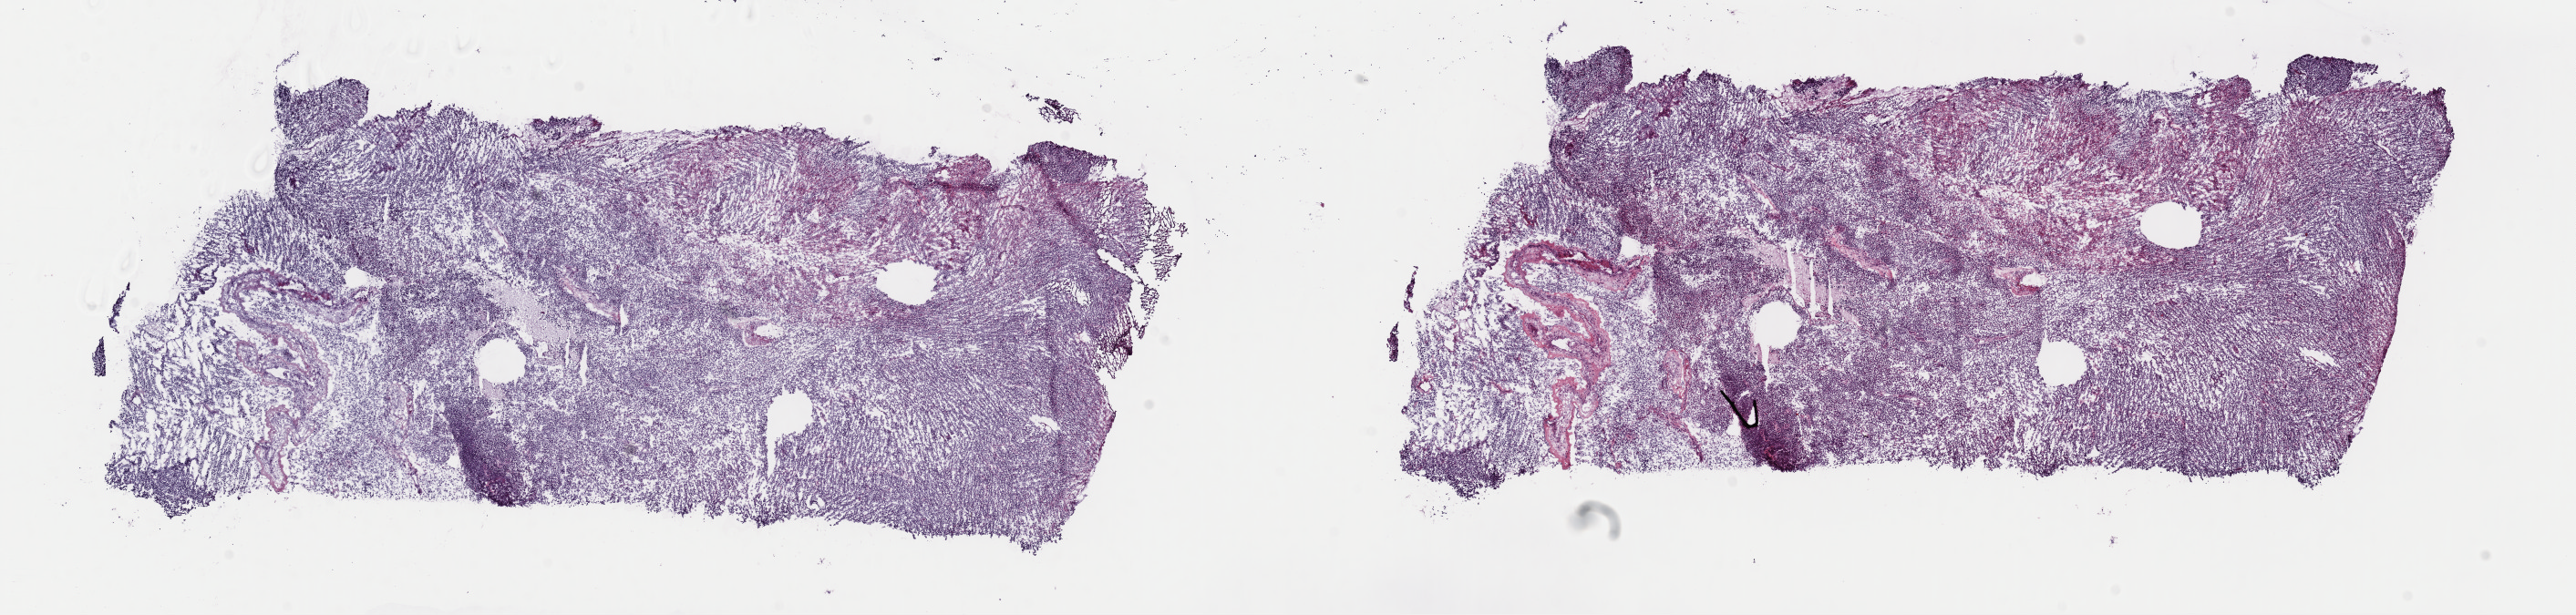
H&E-stained whole-slide image — low-resolution overview of the scanned area, about 22.3 x 5.3 mm (from a 40x scan); frozen section from the top of the tissue portion; primary tumour sample from the brain. Male patient; age at initial diagnosis 68 years. Composition of this section per pathologist review: tumour cells 90%, tumour nuclei 90%, normal cells 0%, stromal cells 5%, necrosis 5%. Inflammatory infiltration, as recorded: lymphocyte infiltration 0%, monocyte infiltration 0%, neutrophil infiltration 0%.
Histologic diagnosis: Glioblastoma.